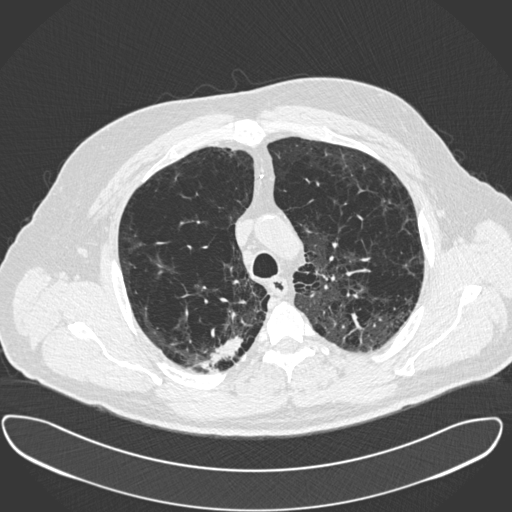
Low-dose screening chest CT, one axial slice. Slice 295 of 385 in the series (ordered by position). Reconstruction kernel B30f. Lung window (W 1500 / L -600 HU). 1 mm slice thickness. 512 × 512 image matrix, field of view 408 × 408 mm.
Outlined on this slice (expert manual segmentation):
- lesion 1 (tumor, upper lobe of right lung): bounding box [x1, y1, x2, y2] px = [194, 336, 243, 372]